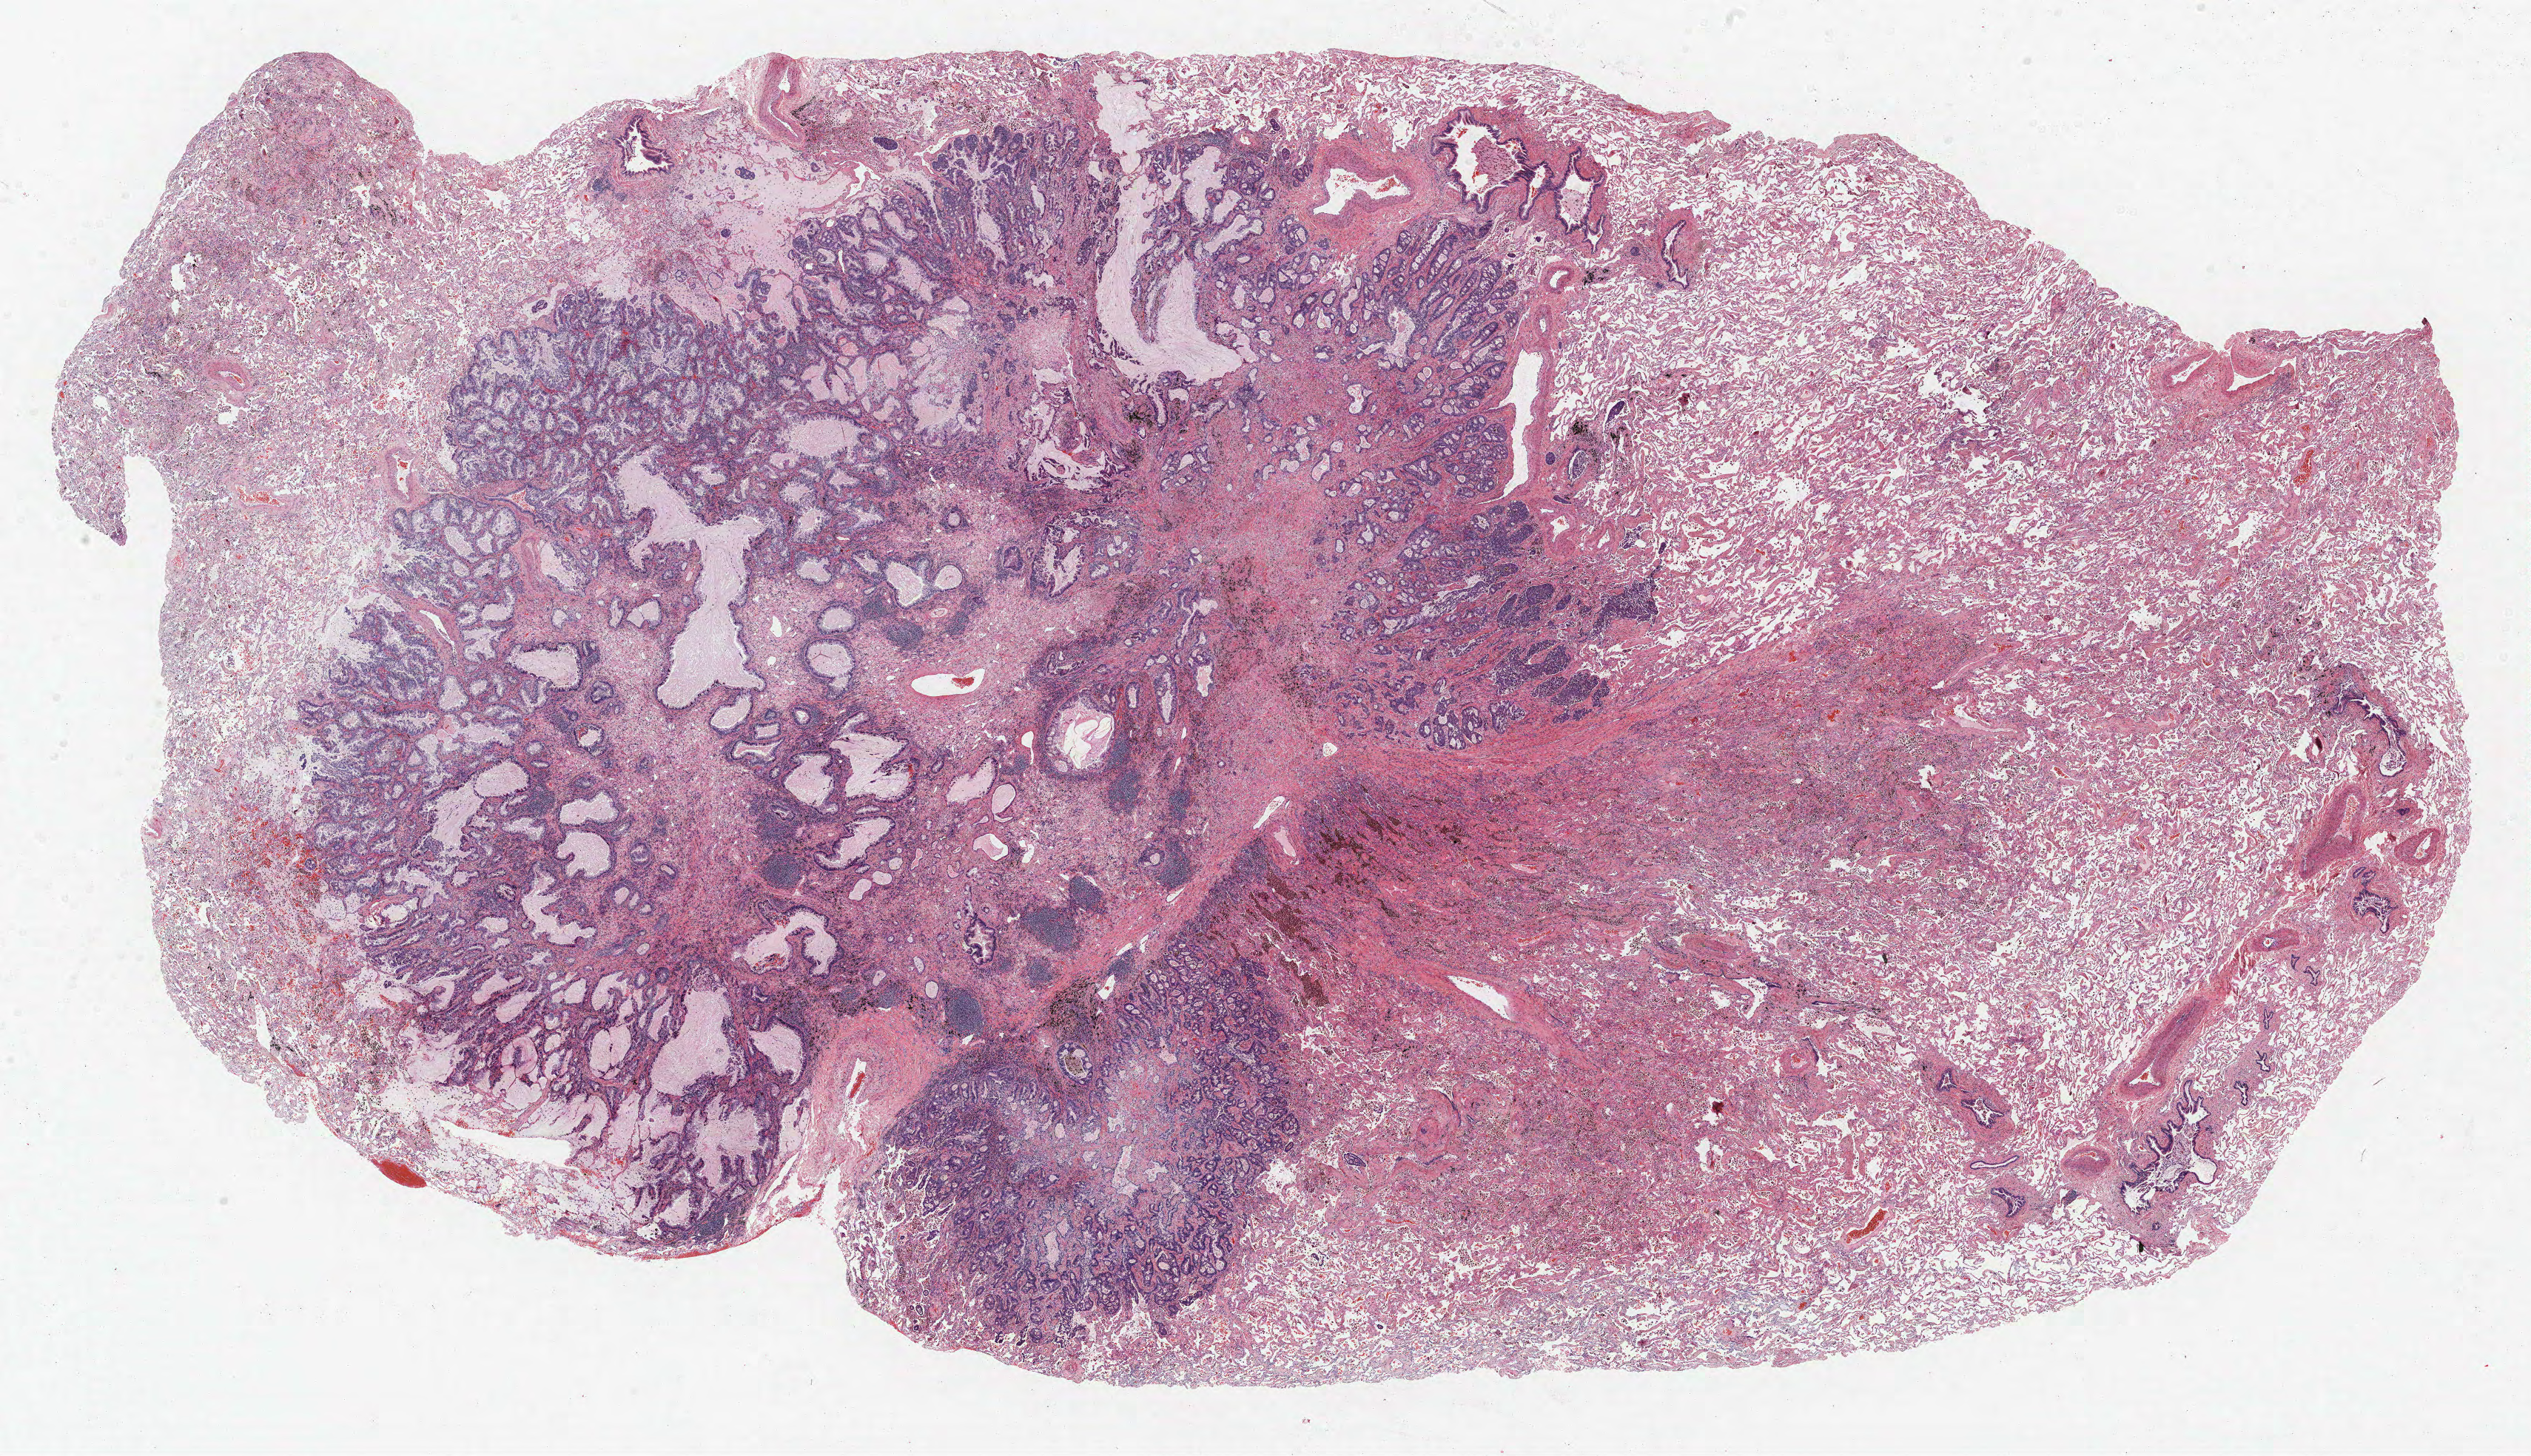
Whole-slide histology image, H&E-stained — a low-resolution overview of the entire scanned area, about 27.4 x 15.7 mm, FFPE section, lung tissue. Male patient, aged 69 at enrolment. Former smoker at enrolment. Grade: well differentiated (G1).
Stage (AJCC 6th edition): IA. ICD-O-3 topography: upper lobe of lung (C34.1). Tumour size (pathology): 17 mm. Participant's lung-cancer diagnosis: Adenocarcinoma, NOS. Primary tumour location (clinical record): right upper lobe.